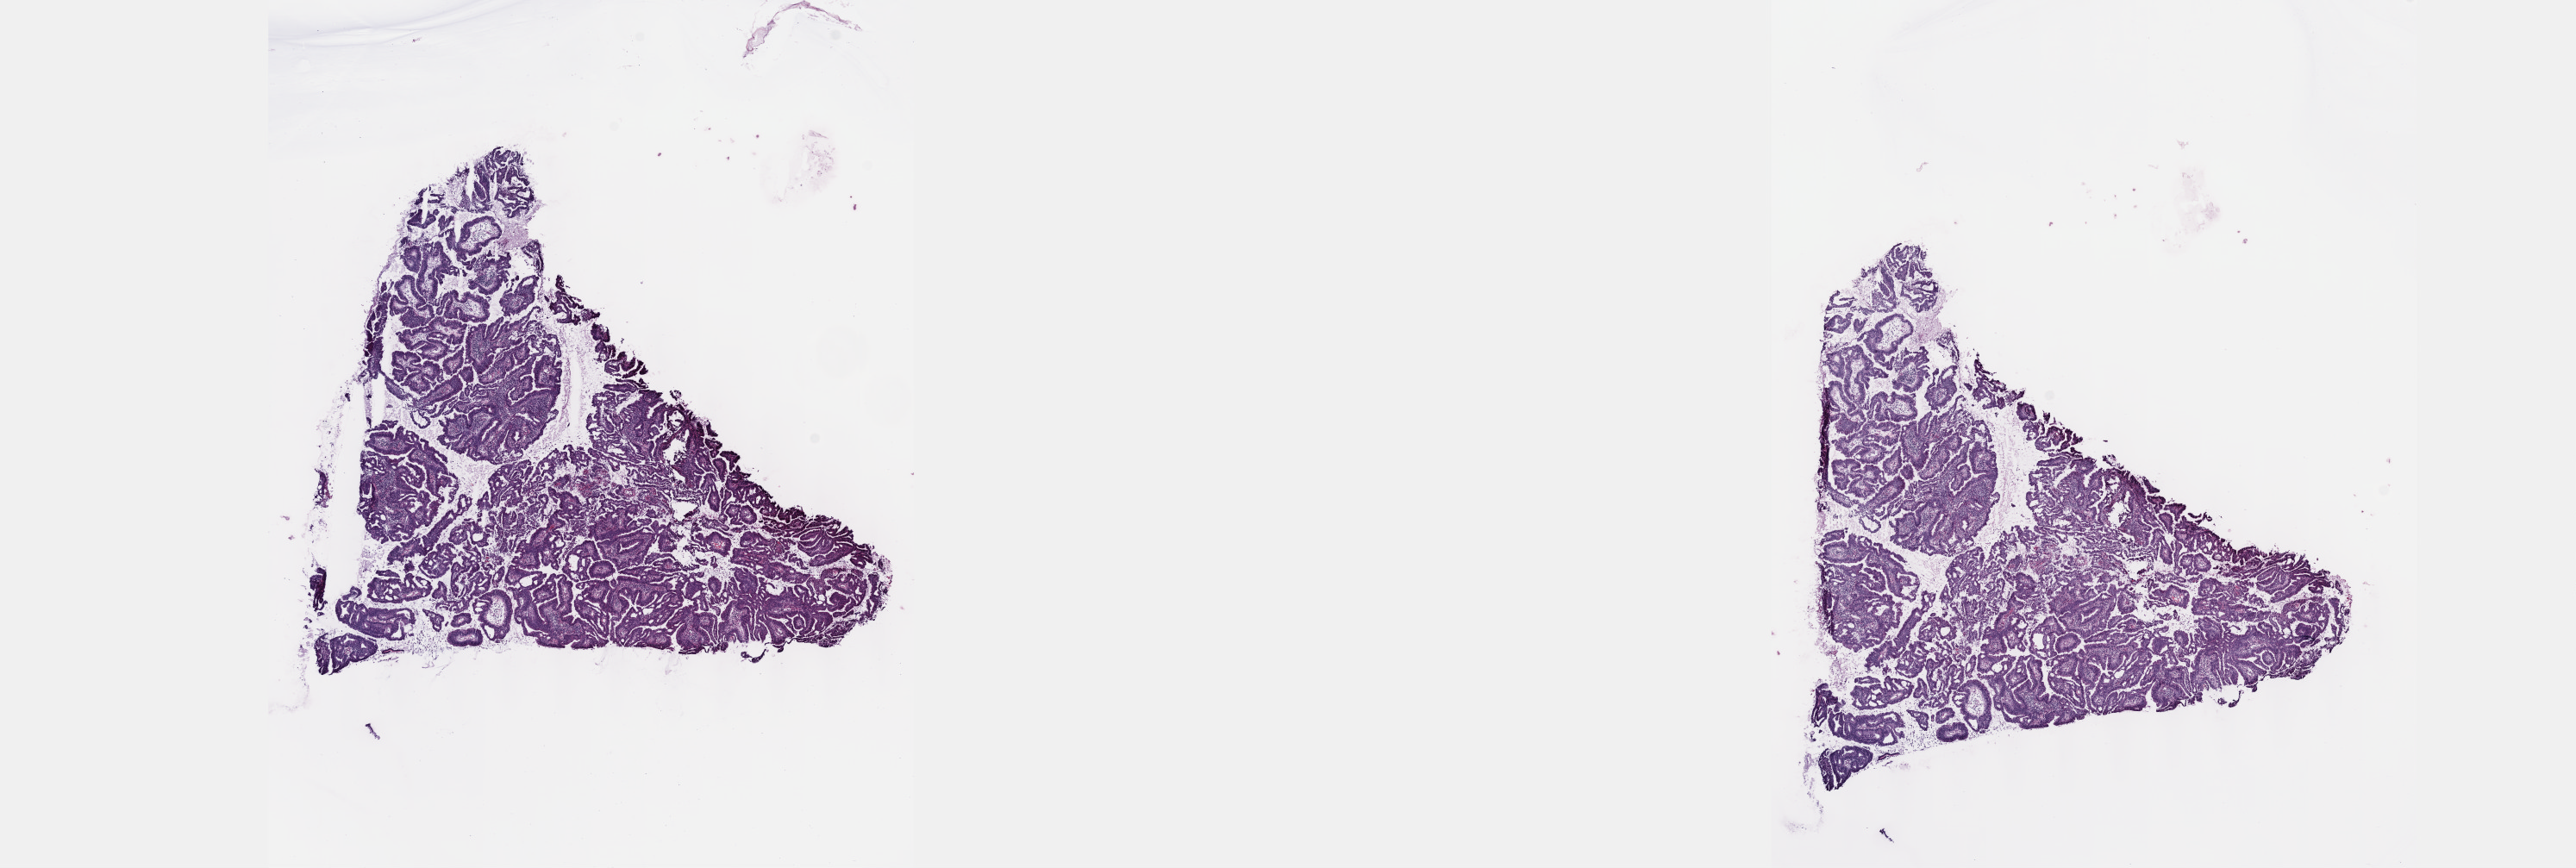
Digitized Hematoxylin and eosin (H&E) stained tissue section (whole slide), a low-resolution overview of the entire scanned area, about 24.1 x 8.1 mm. Frozen section from the top of the tissue portion. Primary tumour sample from the cervix. Female, age 66 years at initial diagnosis. Histologic grade: G2 (moderately differentiated). Slide review estimates, as recorded: tumour cells 70%, tumour nuclei 70%, normal cells 0%, stromal cells 30%, necrosis 0%. Infiltration values recorded for this section: lymphocyte infiltration 40%, monocyte infiltration 20%, neutrophil infiltration 20%.
- lymph nodes positive (case pathology): 0 of 15 examined
- pathologic diagnosis: Mucinous adenocarcinoma, endocervical type
- FIGO stage: IB1